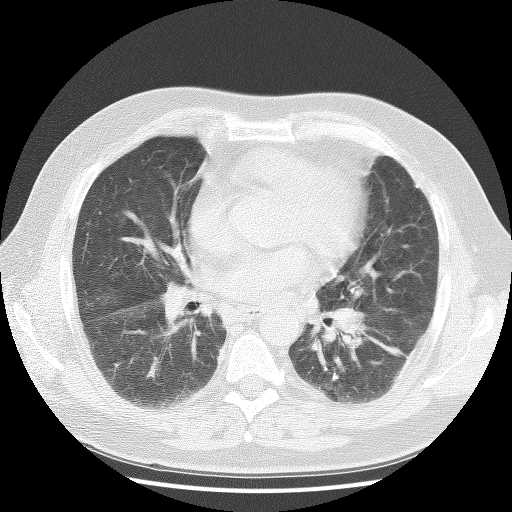
Low-dose screening chest CT, axial slice, baseline screening round, lung window (W 1500 / L -600 HU), 2.5 mm slice thickness, lung (sharp) reconstruction kernel (BONE), 120 kVp. Male, age 59 years at enrolment. Current smoker at enrolment.
Lesion marked by an expert reader, box from (x=306, y=287) to (x=380, y=358) px. The exam's reader record, not a measurement of the box and not confirmed to be the same lesion: non-calcified nodule or mass ≥4 mm, right upper lobe, 4 × 4 mm, soft tissue attenuation. Note: the box lies in the patient's left hemithorax on this image, whereas the reader's record names the right lung; they may be different findings. Lung cancer was diagnosed 20 days after this screen: non-small cell carcinoma, left hilum, stage IV (AJCC 6th edition).